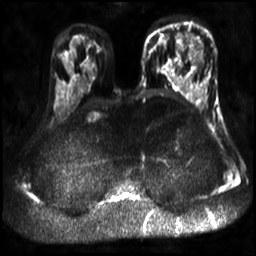
Breast MRI, one axial slice. Slice 17 of 30 in the series (ordered by position). Diffusion-weighted series; image 2 of 4 stored at this slice position (different b-values; order by instance number). 3 T. 4 mm slice thickness. 256 × 256 image matrix, field of view 320 × 320 mm. Female patient.
Outlined on this slice (manually delineated by an expert):
- tumour on diffusion-weighted imaging: bounding box <188,33,205,67> (left, top, right, bottom; pixels)